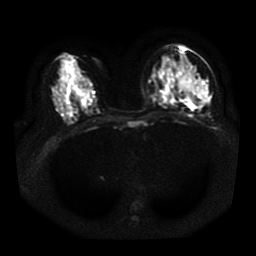
Breast MRI, one axial slice; diffusion-weighted series; image 2 of 4 stored at this slice position (different b-values; order by instance number); 1.5 T; 5 mm slice thickness; 256 × 256 image matrix, field of view 330 × 330 mm. Female patient.
Annotated regions visible in this slice (outlined manually by an expert reader):
- tumour on diffusion-weighted imaging: bounding box [x1, y1, x2, y2] px = [169, 59, 205, 106]